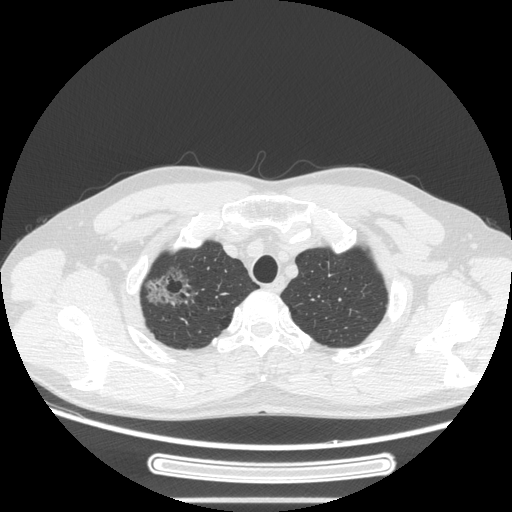
Chest CT, one axial slice. Slice 228 of 269 in the series (ordered by position). Reconstruction kernel STANDARD. 120 kVp. Lung window (W 1500 / L -600 HU). 1.25 mm slice thickness. 512 × 512 image matrix, field of view 382 × 382 mm. Male patient, age 53 years. Case-level facts recorded for this patient, not image findings: clinical TNM (as recorded): T1c N0 M0; histopathological grade: G2.
Annotated regions visible in this slice (bounding box drawn by a radiologist):
- lung tumour (recorded histology: adenocarcinoma): box from (x=136, y=261) to (x=196, y=313) px